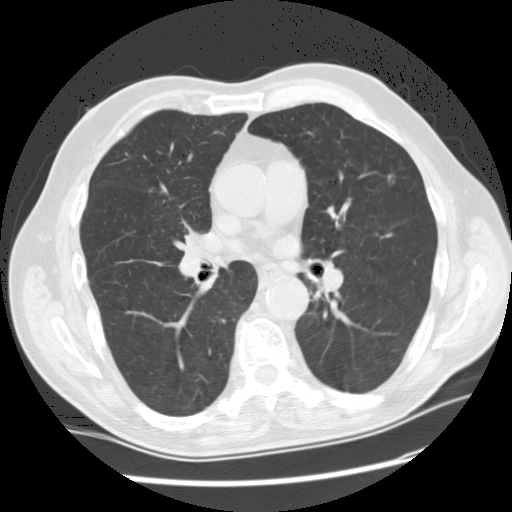
Low-dose screening chest CT, axial slice; third annual screen; lung window (W 1500 / L -600 HU); standard (soft-tissue) reconstruction kernel (STANDARD); 120 kVp. Male, age 71 years at enrolment. Current smoker at enrolment.
• Lesion marked by an expert reader, bounding box (x1, y1, x2, y2) in pixels: (360, 162, 413, 207).
• The screening reader recorded 2 non-calcified nodules or masses ≥4 mm on this exam (lingula, left upper lobe); which of them this box marks is not recorded.
• Official screen result: positive, other.
• Later outcome: lung cancer diagnosed 100 days after this screen — adenocarcinoma, NOS, left upper lobe, moderately differentiated (G2), stage IA (AJCC 6th edition), 10 mm at pathology.